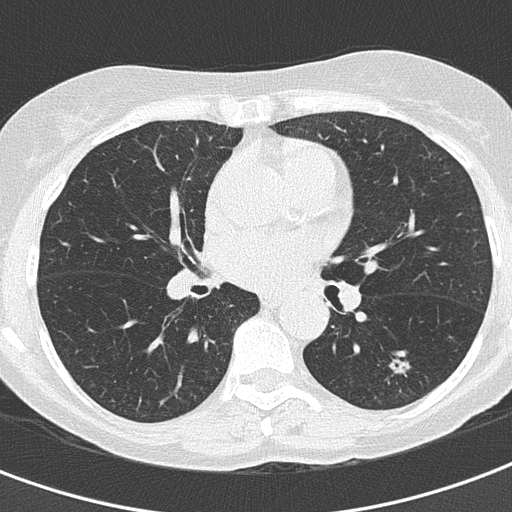
Chest CT (low-dose screening protocol), one axial image. Second screening round (one year after baseline). Lung window (W 1500 / L -600 HU). 2 mm slice thickness. 120 kVp. Slice 75 of 155 in the series. Female participant, aged 60 years at enrolment.
• Lesion marked by an expert reader, bounding box <378,348,414,378> (left, top, right, bottom; pixels).
• Reader record for this screening exam (exam-level; its link to the box is not recorded): non-calcified nodule or mass ≥4 mm, left lower lobe, 10 × 9 mm, soft tissue attenuation.
• Later outcome: lung cancer diagnosed 64 days after this screen — adenocarcinoma, NOS, left lower lobe, well differentiated (G1), stage IA (AJCC 6th edition), 15 mm at pathology.